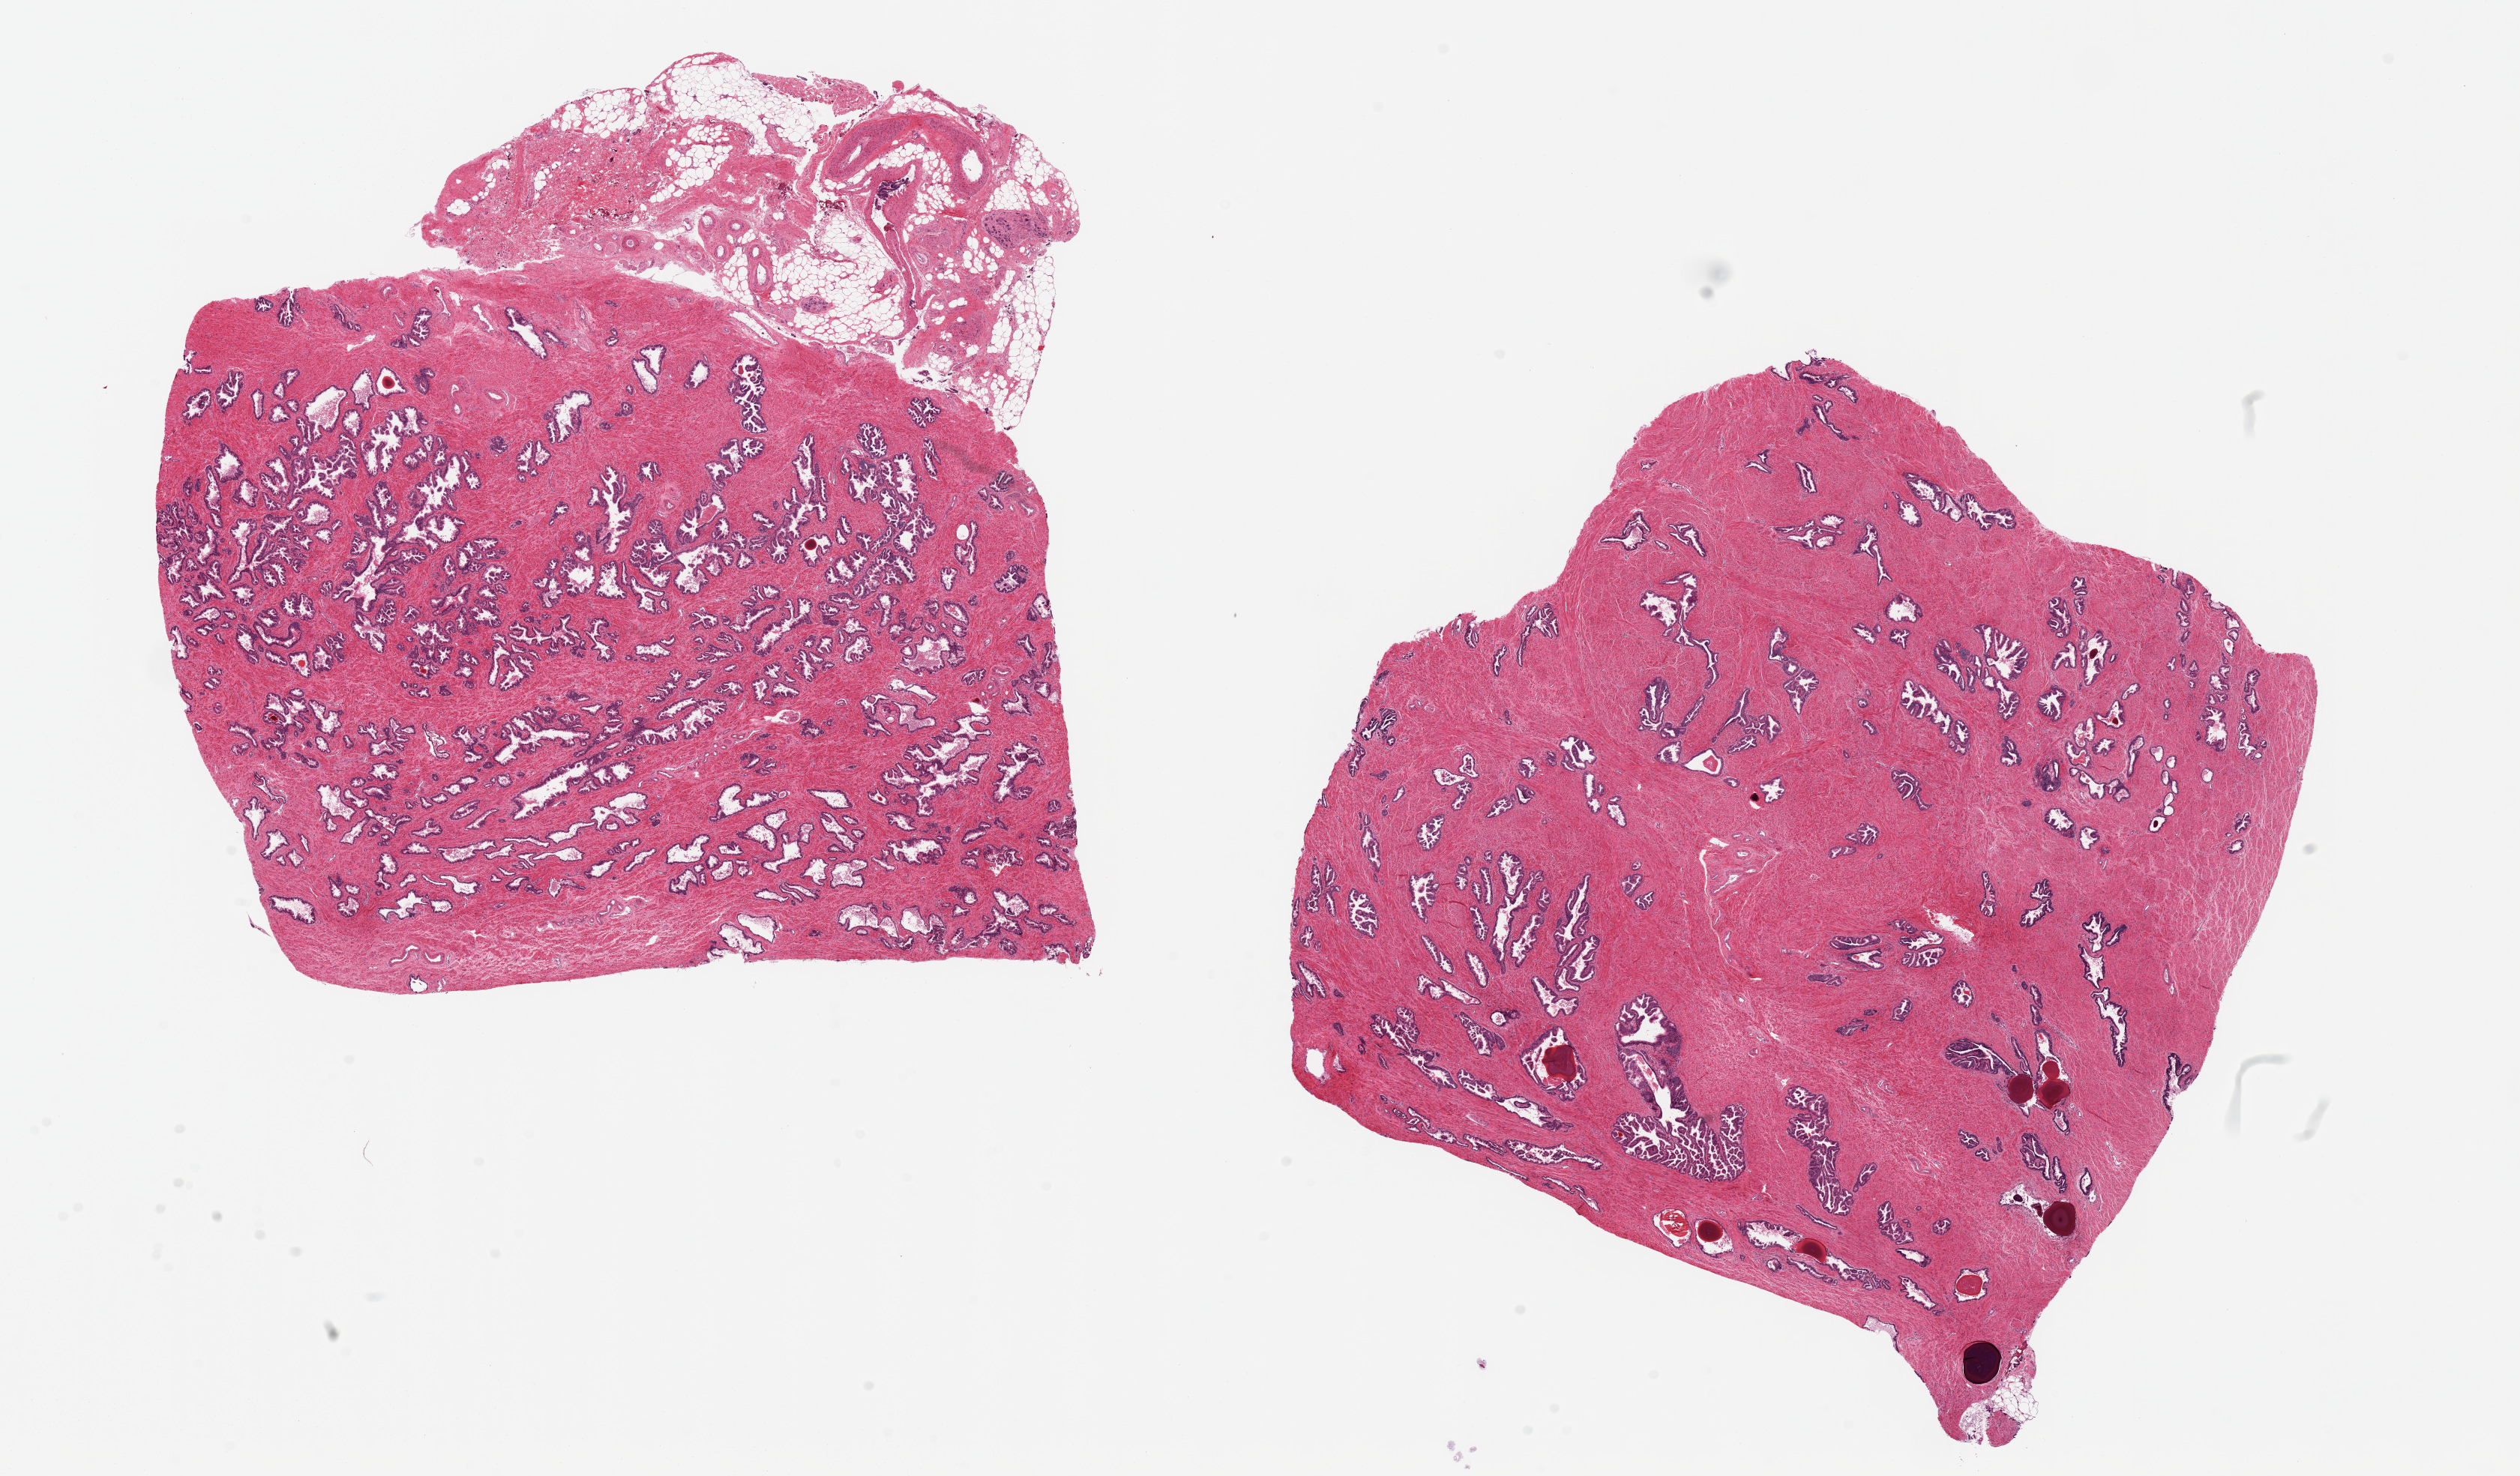
Whole-slide image, hematoxylin and eosin (H&E) stain, shown as a low-resolution overview of the whole scanned area (about 26.6 x 15.6 mm); PAXgene-fixed, paraffin-embedded tissue; sampled site (target tissue): prostate; donor tissue sample. Donor: male.
• review note (as recorded): 2 pieces, diffuse glandular hyperplasia; Large adherent 6mm fatty nubbin attached to one aliquot/